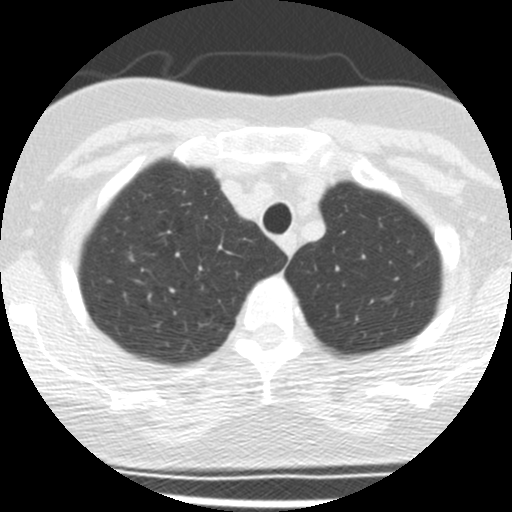
Low-dose screening chest CT, one axial slice; slice 154 of 190 in the series (ordered by position); reconstruction kernel STANDARD; 120 kVp; lung window (W 1500 / L -600 HU); 512 × 512 image matrix.
Annotated regions visible in this slice (outlined manually by an expert reader):
- lesion 1 (tumor, upper lobe of right lung): bounding box <129,254,133,260> (left, top, right, bottom; pixels)